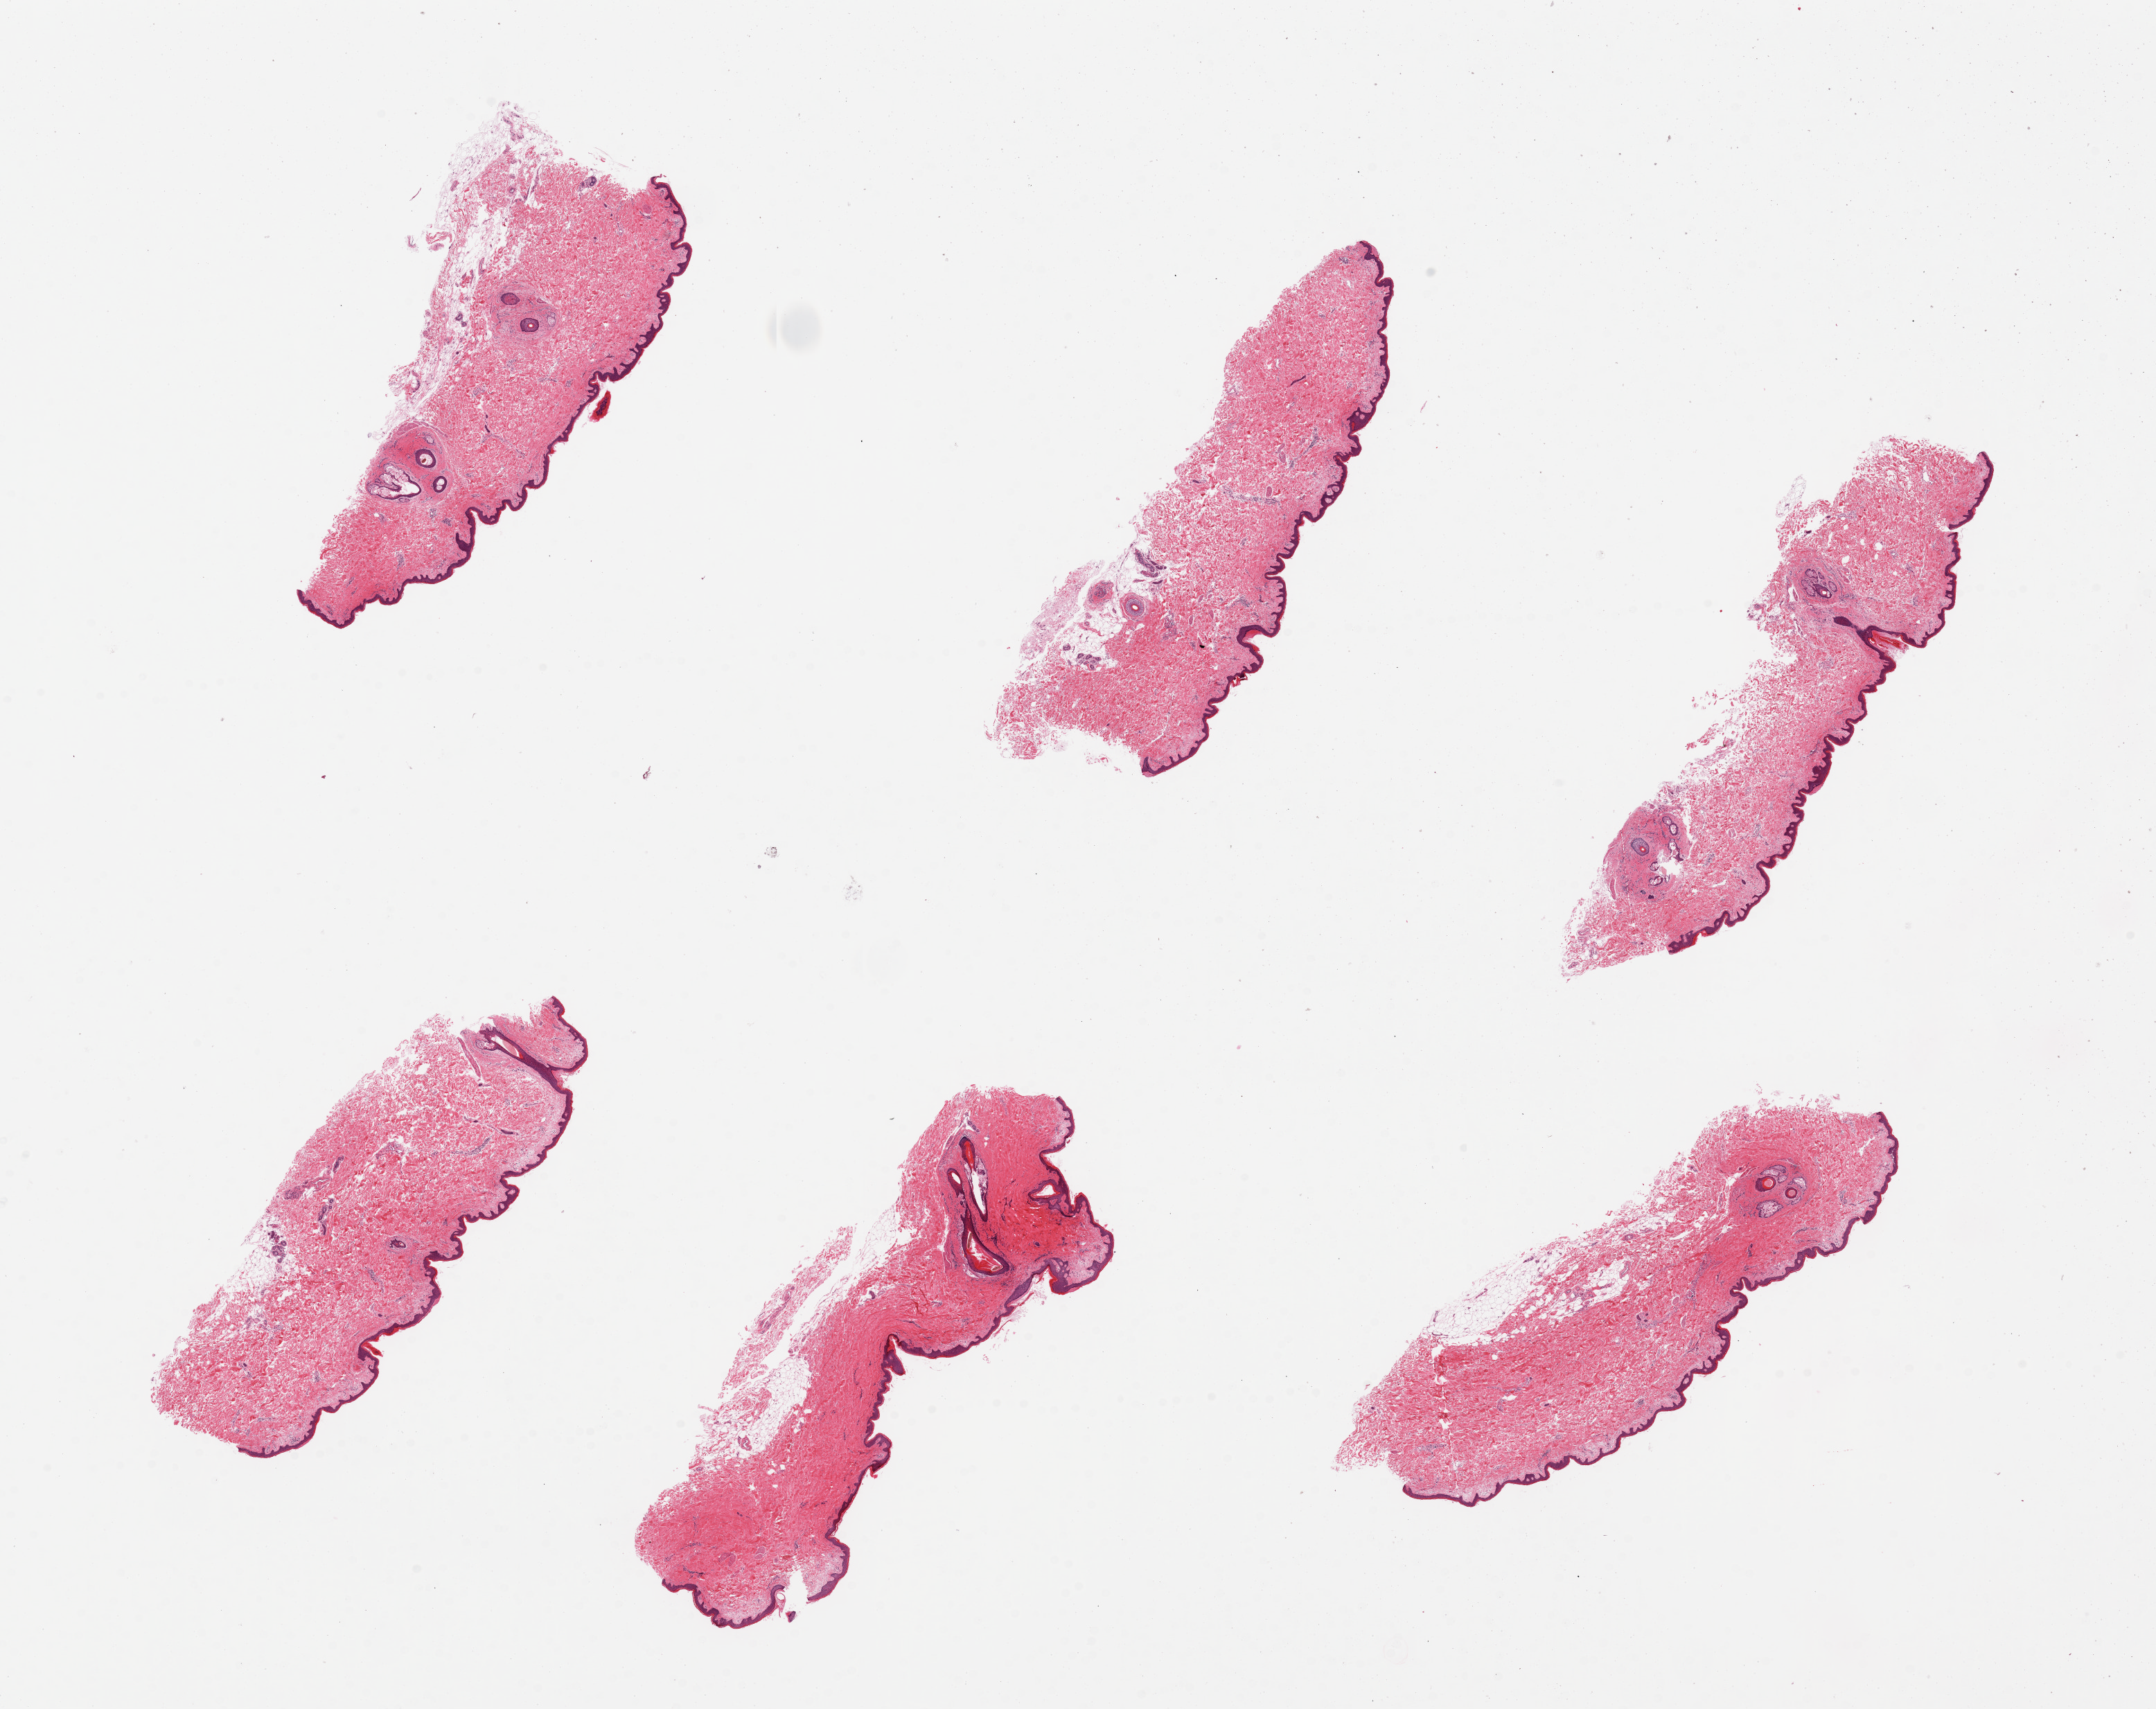
Whole-slide image, hematoxylin and eosin (H&E) stain, brightfield — whole scanned area (about 24.6 x 19.5 mm, acquisition: 20x scan) shown as a low-resolution overview, PAXgene-fixed, paraffin-embedded tissue, target tissue: skin of suprapubic region, tissue donor sample. Donor sex: male.
Review note (as recorded): 6 pieces.